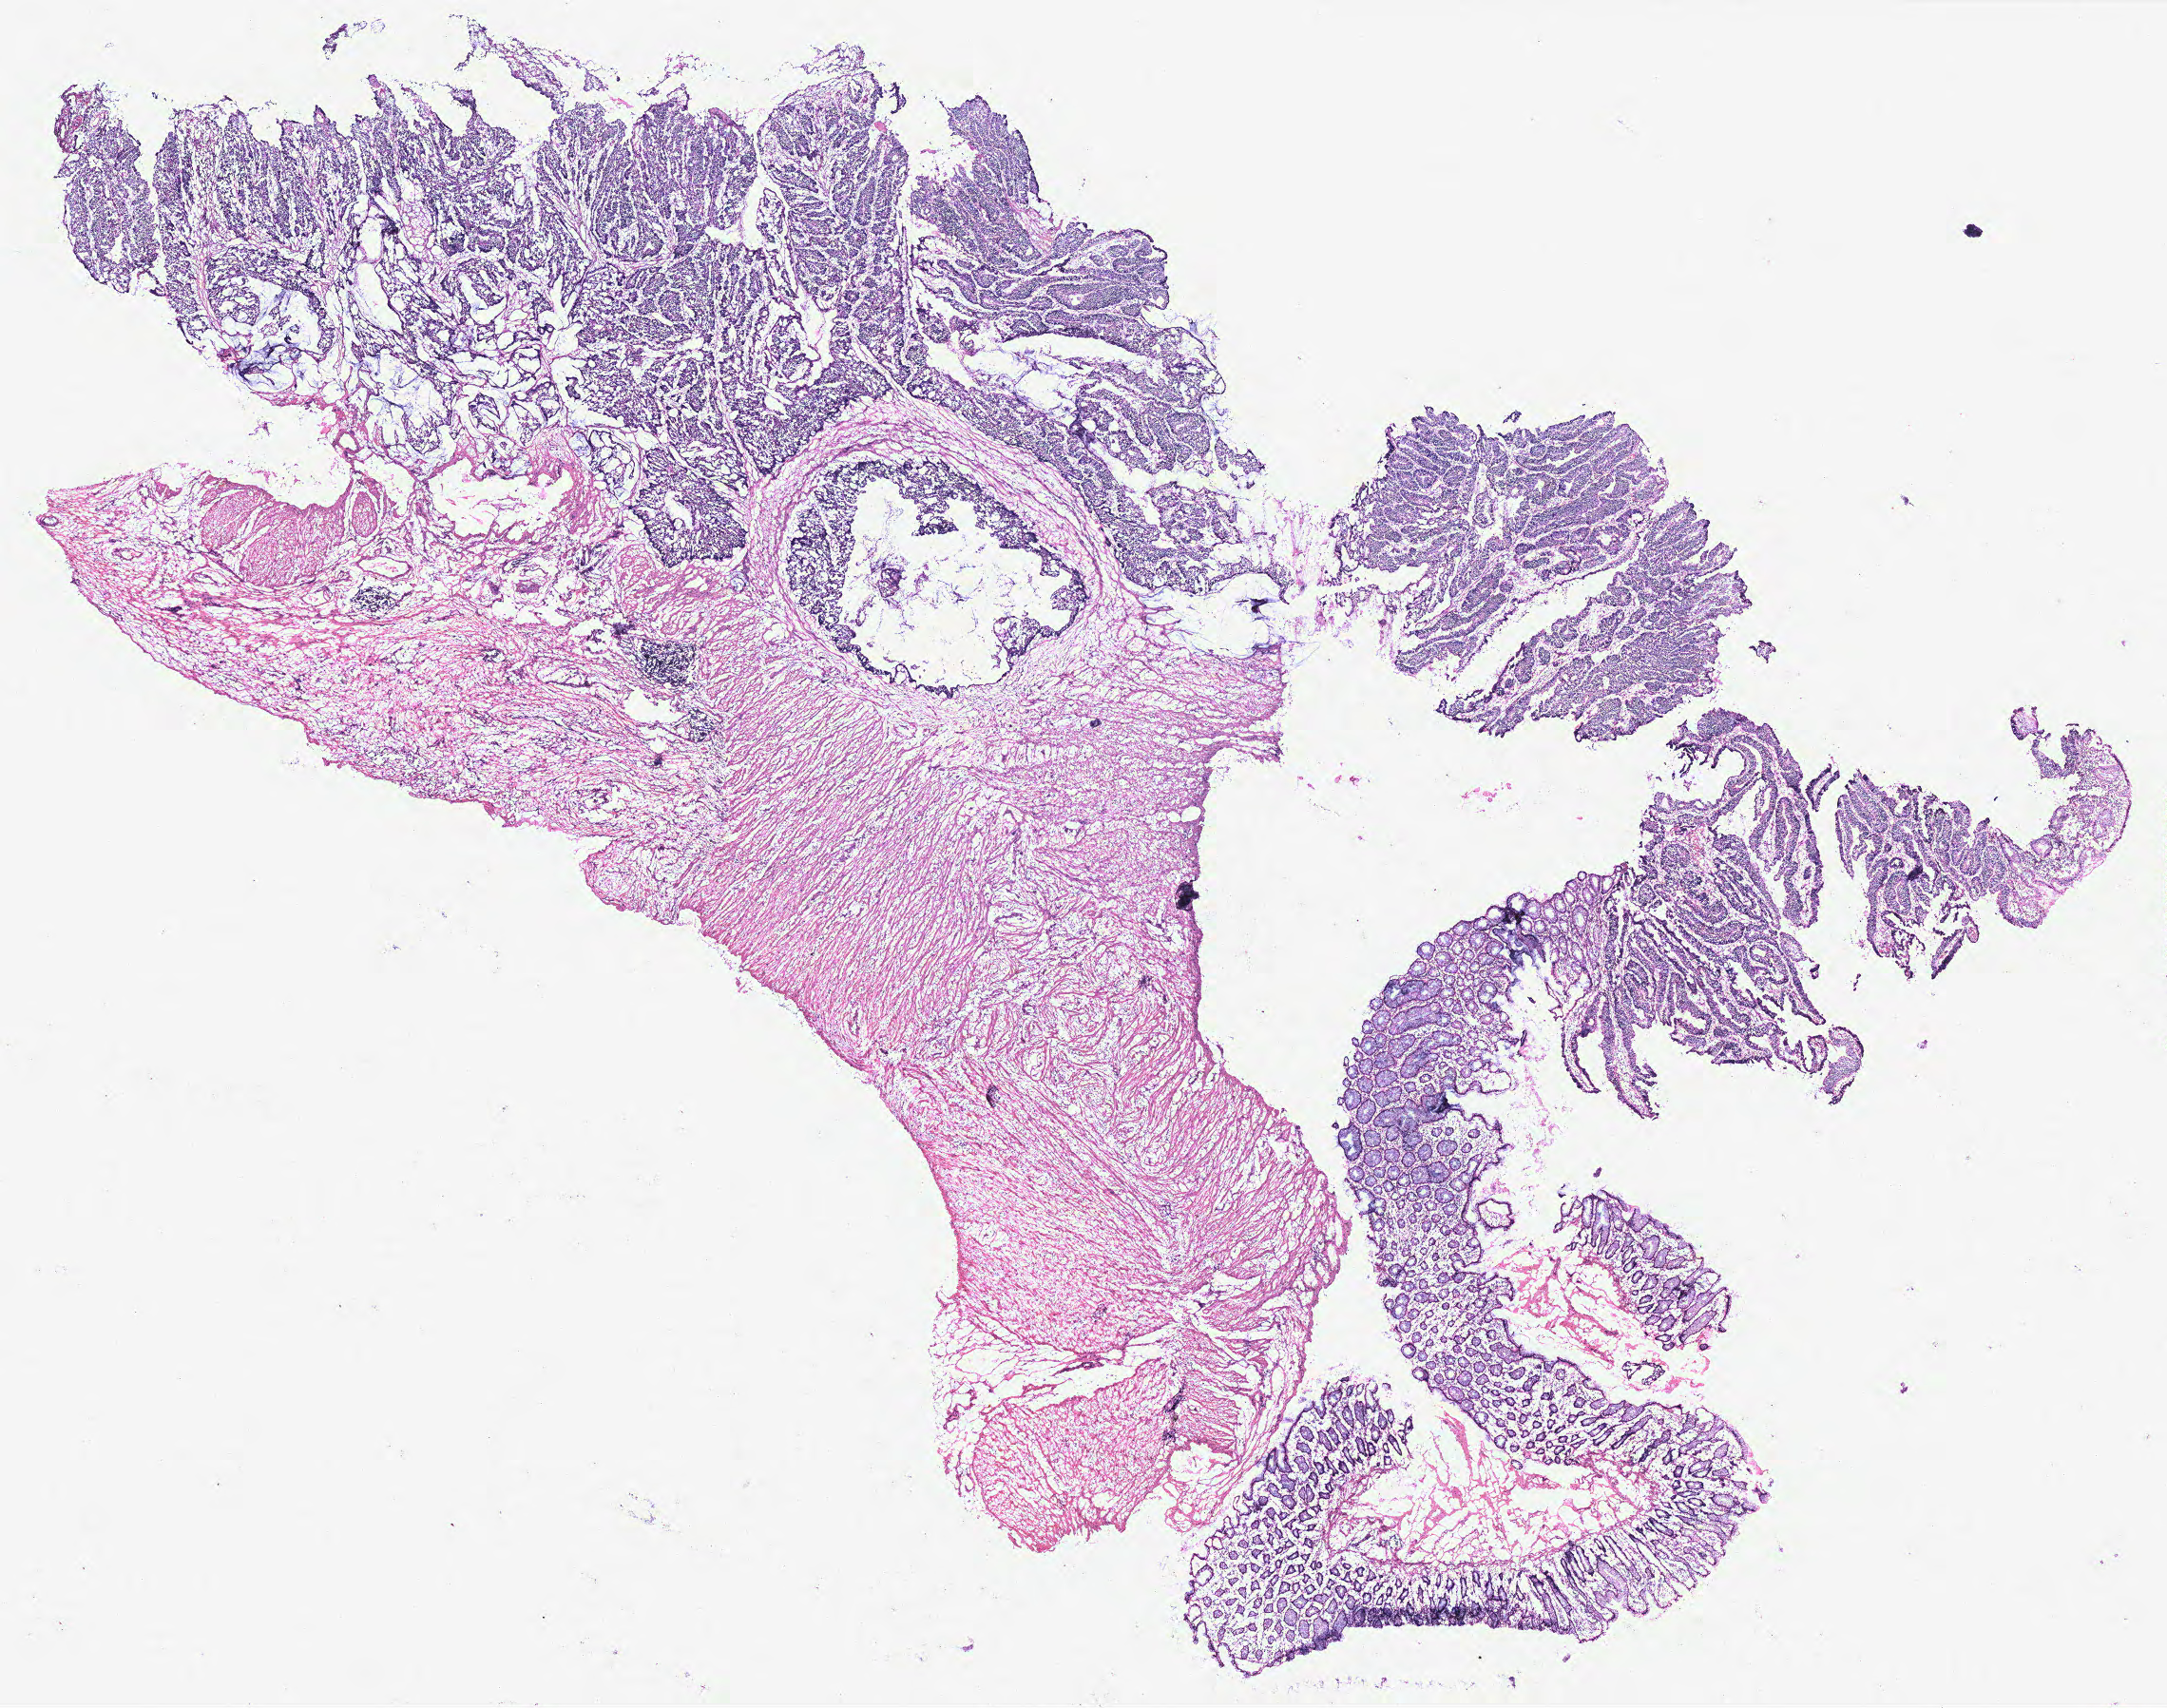
Whole-slide histology image, H&E-stained — low-resolution overview of the scanned area, about 18.2 x 14.4 mm; colon, tissue type not recorded.
- patient diagnosis (cohort enrolment): colon cancer (colon)